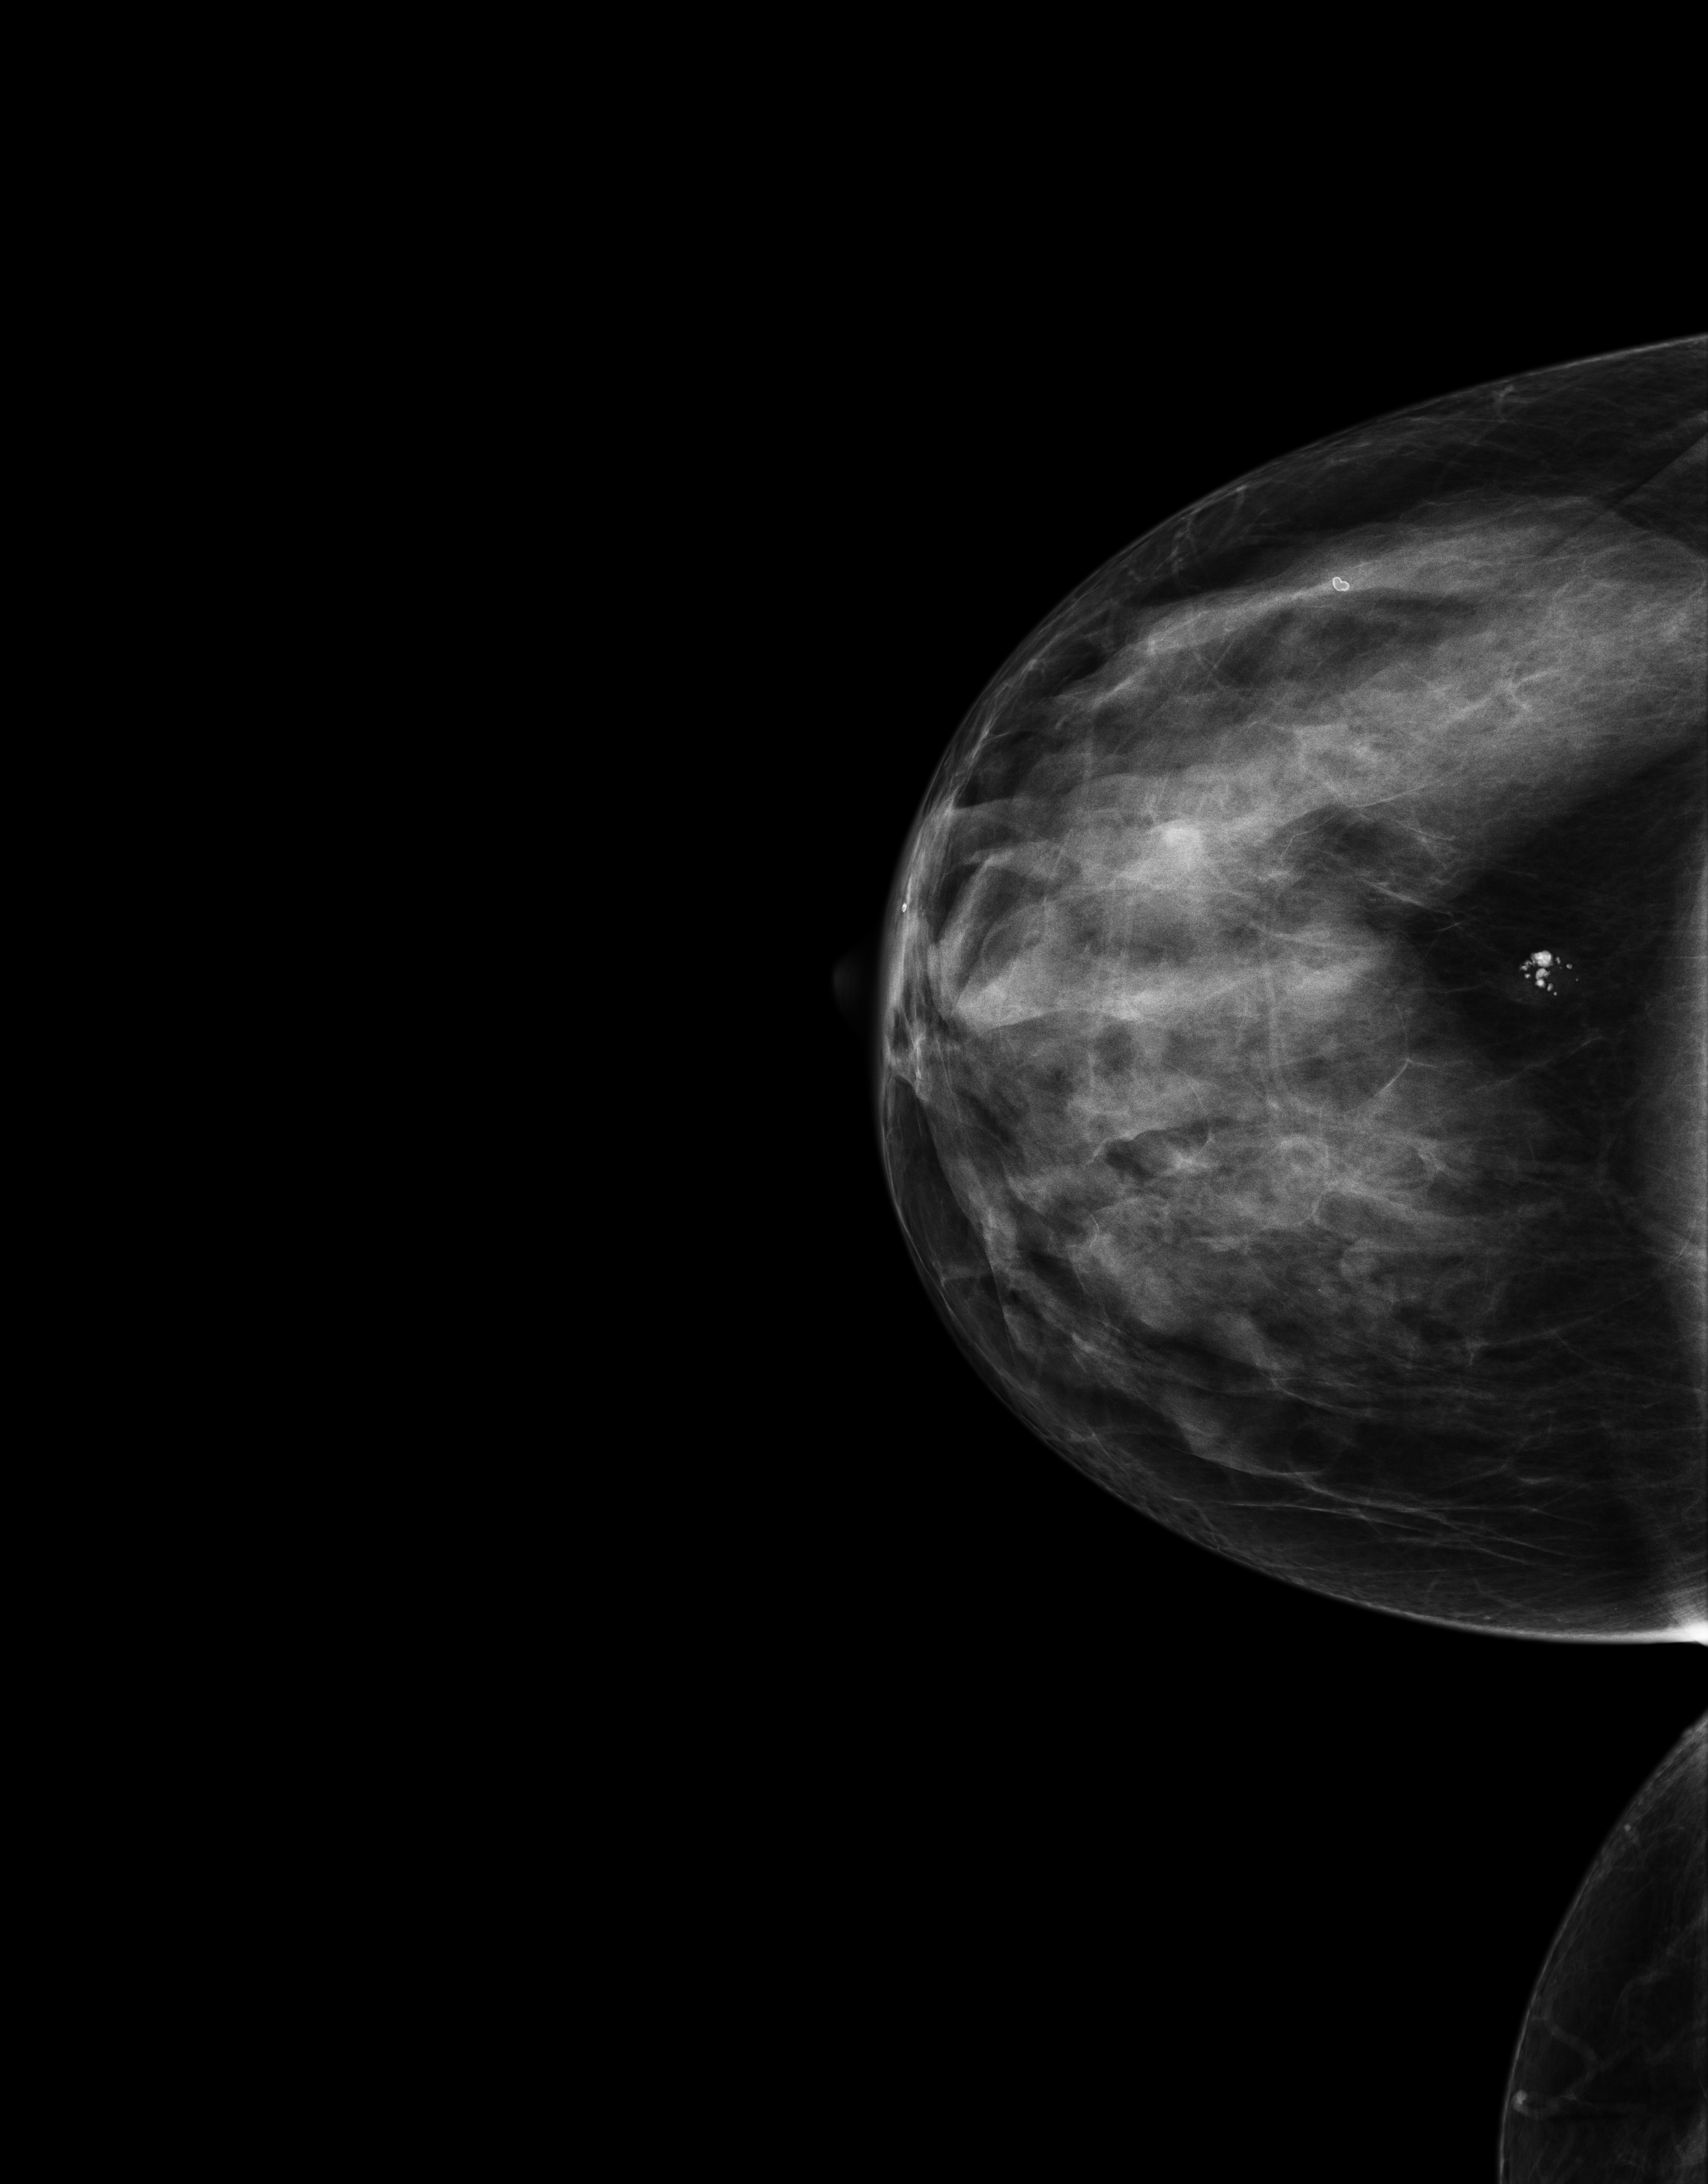
Screening examination, compressed breast thickness 53 mm, system: Senographe Essential ADS_56.21.3. Female patient, age 61 years.
Image type: full-field digital mammogram. Breast: right. Projection: CC view.